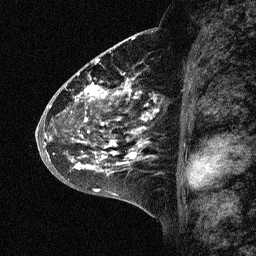
Breast MRI (dynamic contrast-enhanced), one sagittal slice; dynamic contrast-enhanced study with each time point stored as its own series, time point 2 of 3 at this slice position (early post-contrast, ordered by acquisition time); 1.5 T; TE 4.5 ms, TR 11 ms; 2.06 mm slice thickness; 256 × 256 image matrix, field of view 200 × 200 mm. Female patient, age 46 years. Case-level facts recorded for this patient, not image findings: setting: breast cancer imaged before/during neoadjuvant chemotherapy; receptor status: HER2-positive.
Outlined on this slice (semi-automatic segmentation, software-assisted and operator-edited):
- analysis volume of interest (the breast-tissue region the enhancement analysis was run in; not a lesion): bounding box <43,72,173,177> (left, top, right, bottom; pixels)
- tumour enhancement mask (voxels above the 90 % enhancement threshold inside the analysis volume of interest): <45,73,156,173>